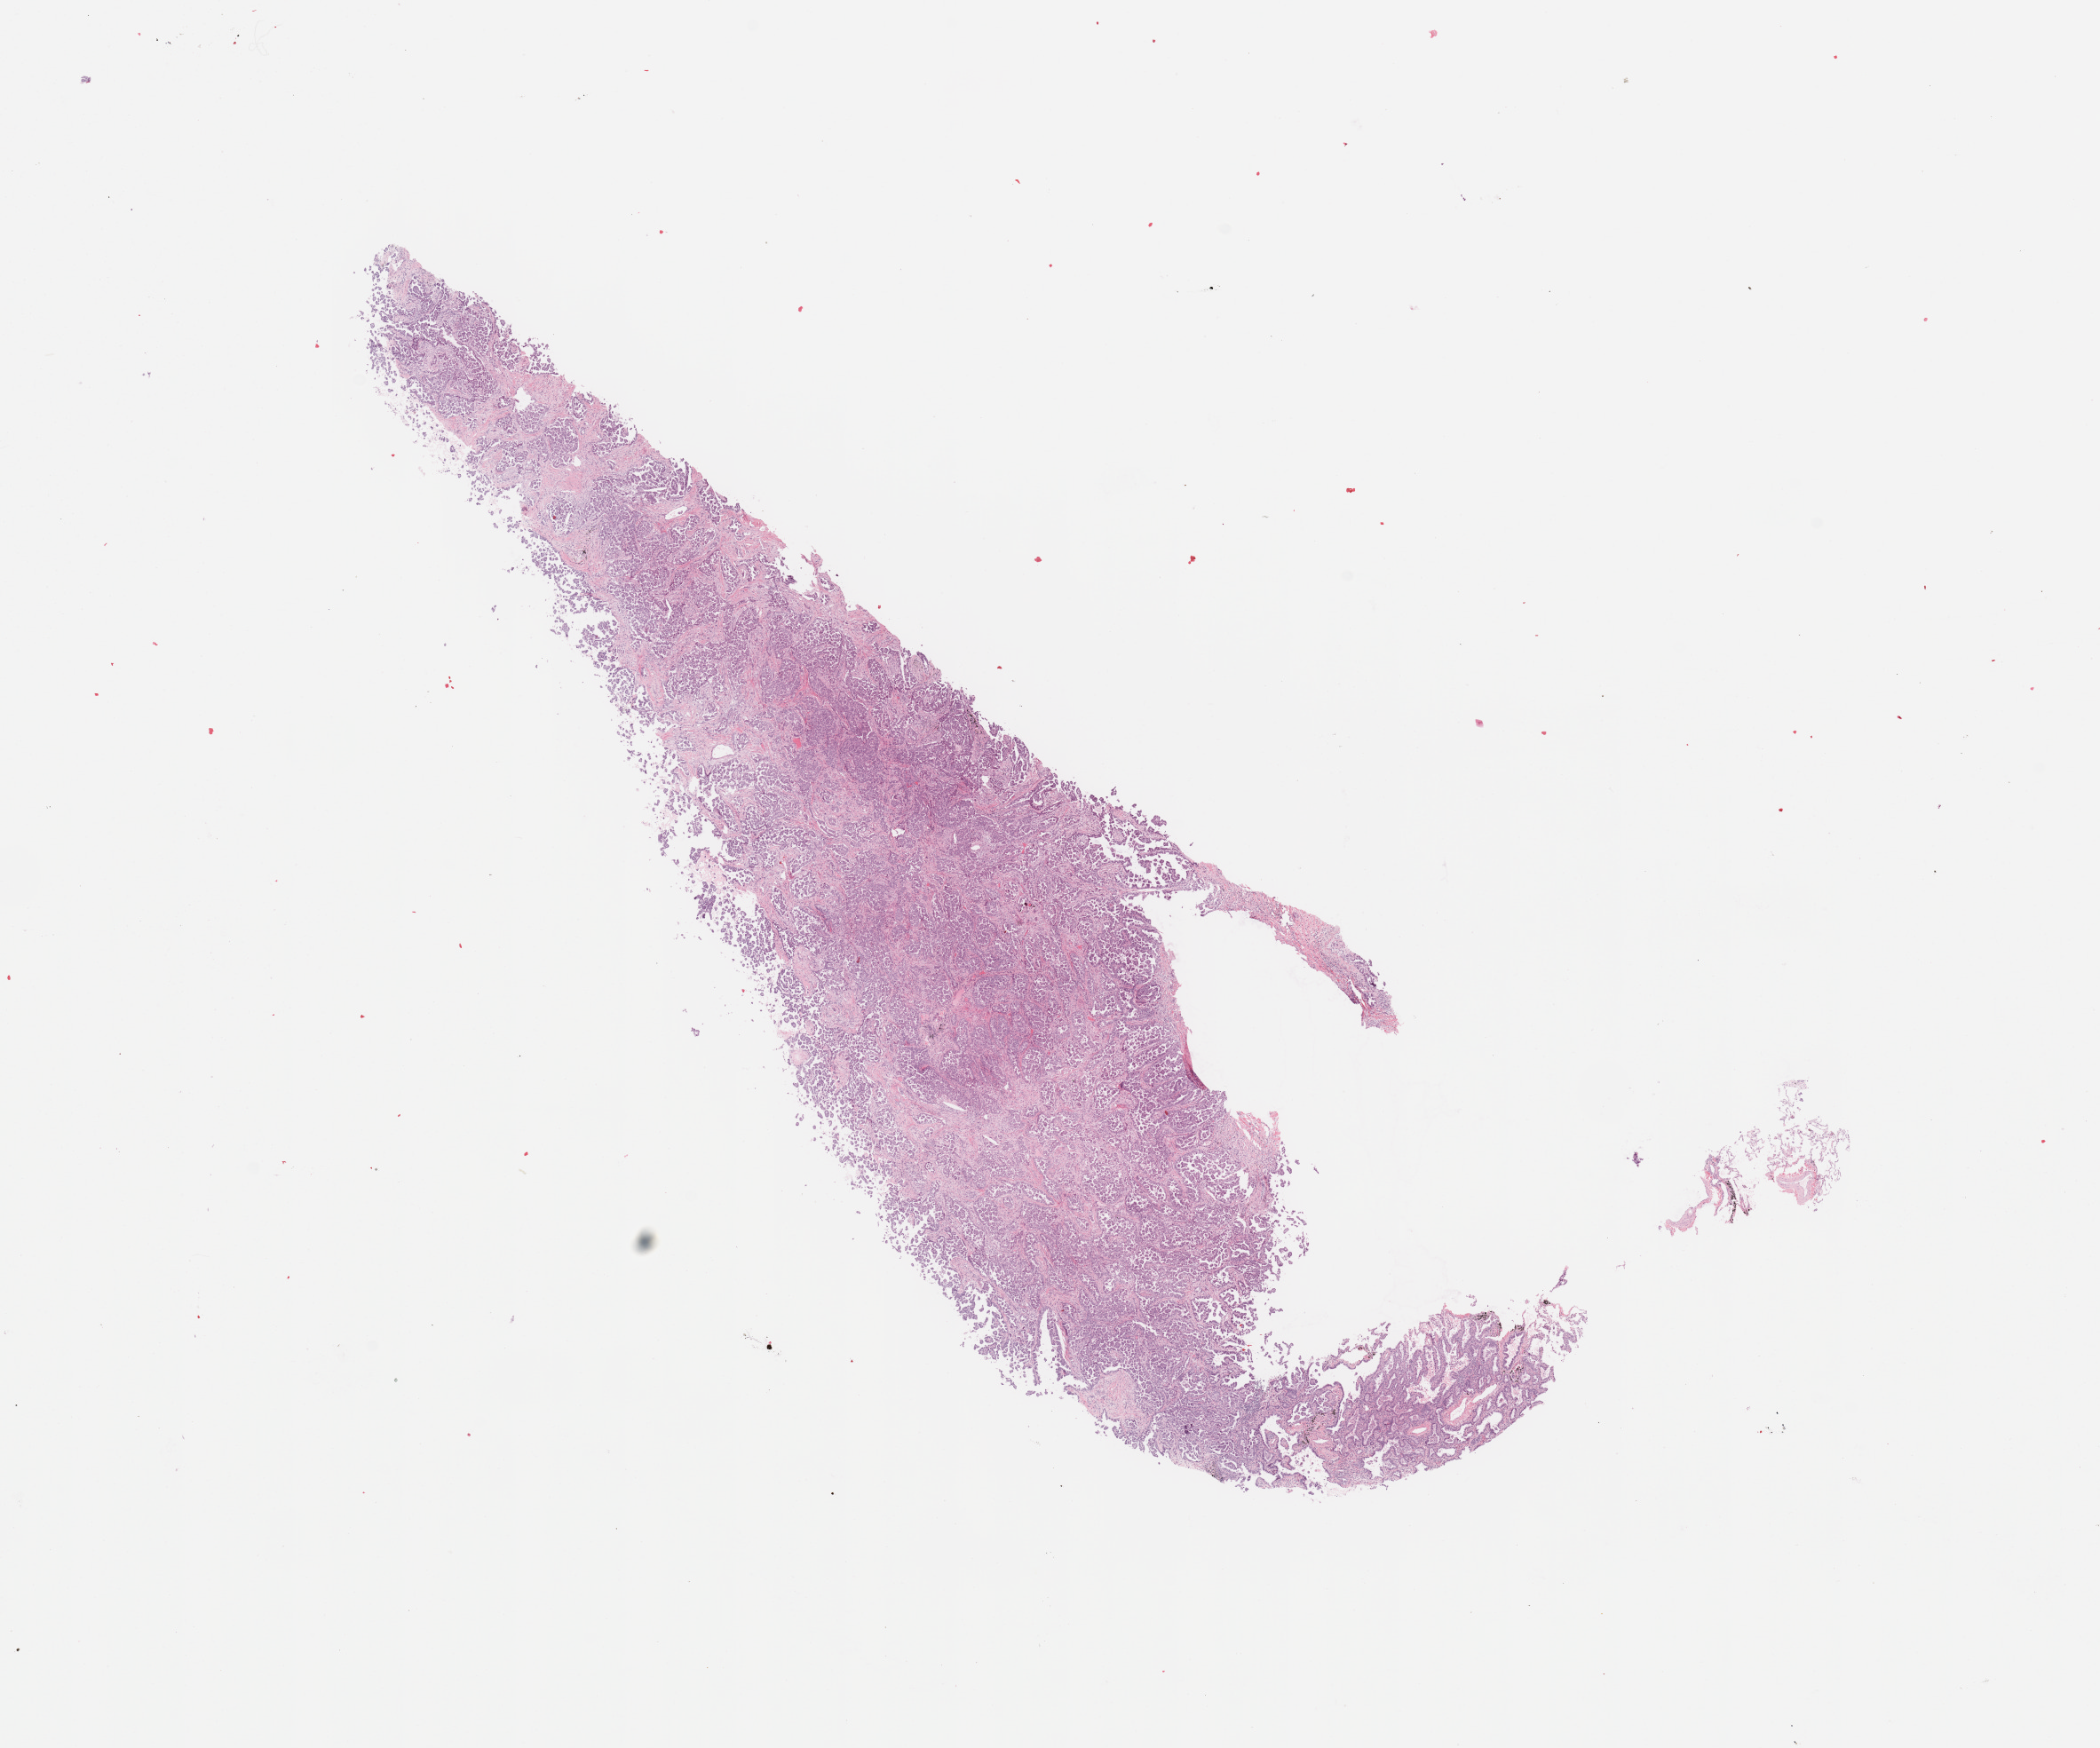
H&E-stained whole-slide image, low-resolution overview of the scanned area, about 18.7 x 15.6 mm (slide scanned at 20x). Tumour tissue sample, sampled site: lung. 68-year-old male patient. Histologic grade: G3 (poorly differentiated). Pathologist review of this section (percent, as recorded): tumour nuclei 80%, necrosis 3%.
AJCC pathologic stage: IIIA. Diagnosis: Adenocarcinoma, NOS.